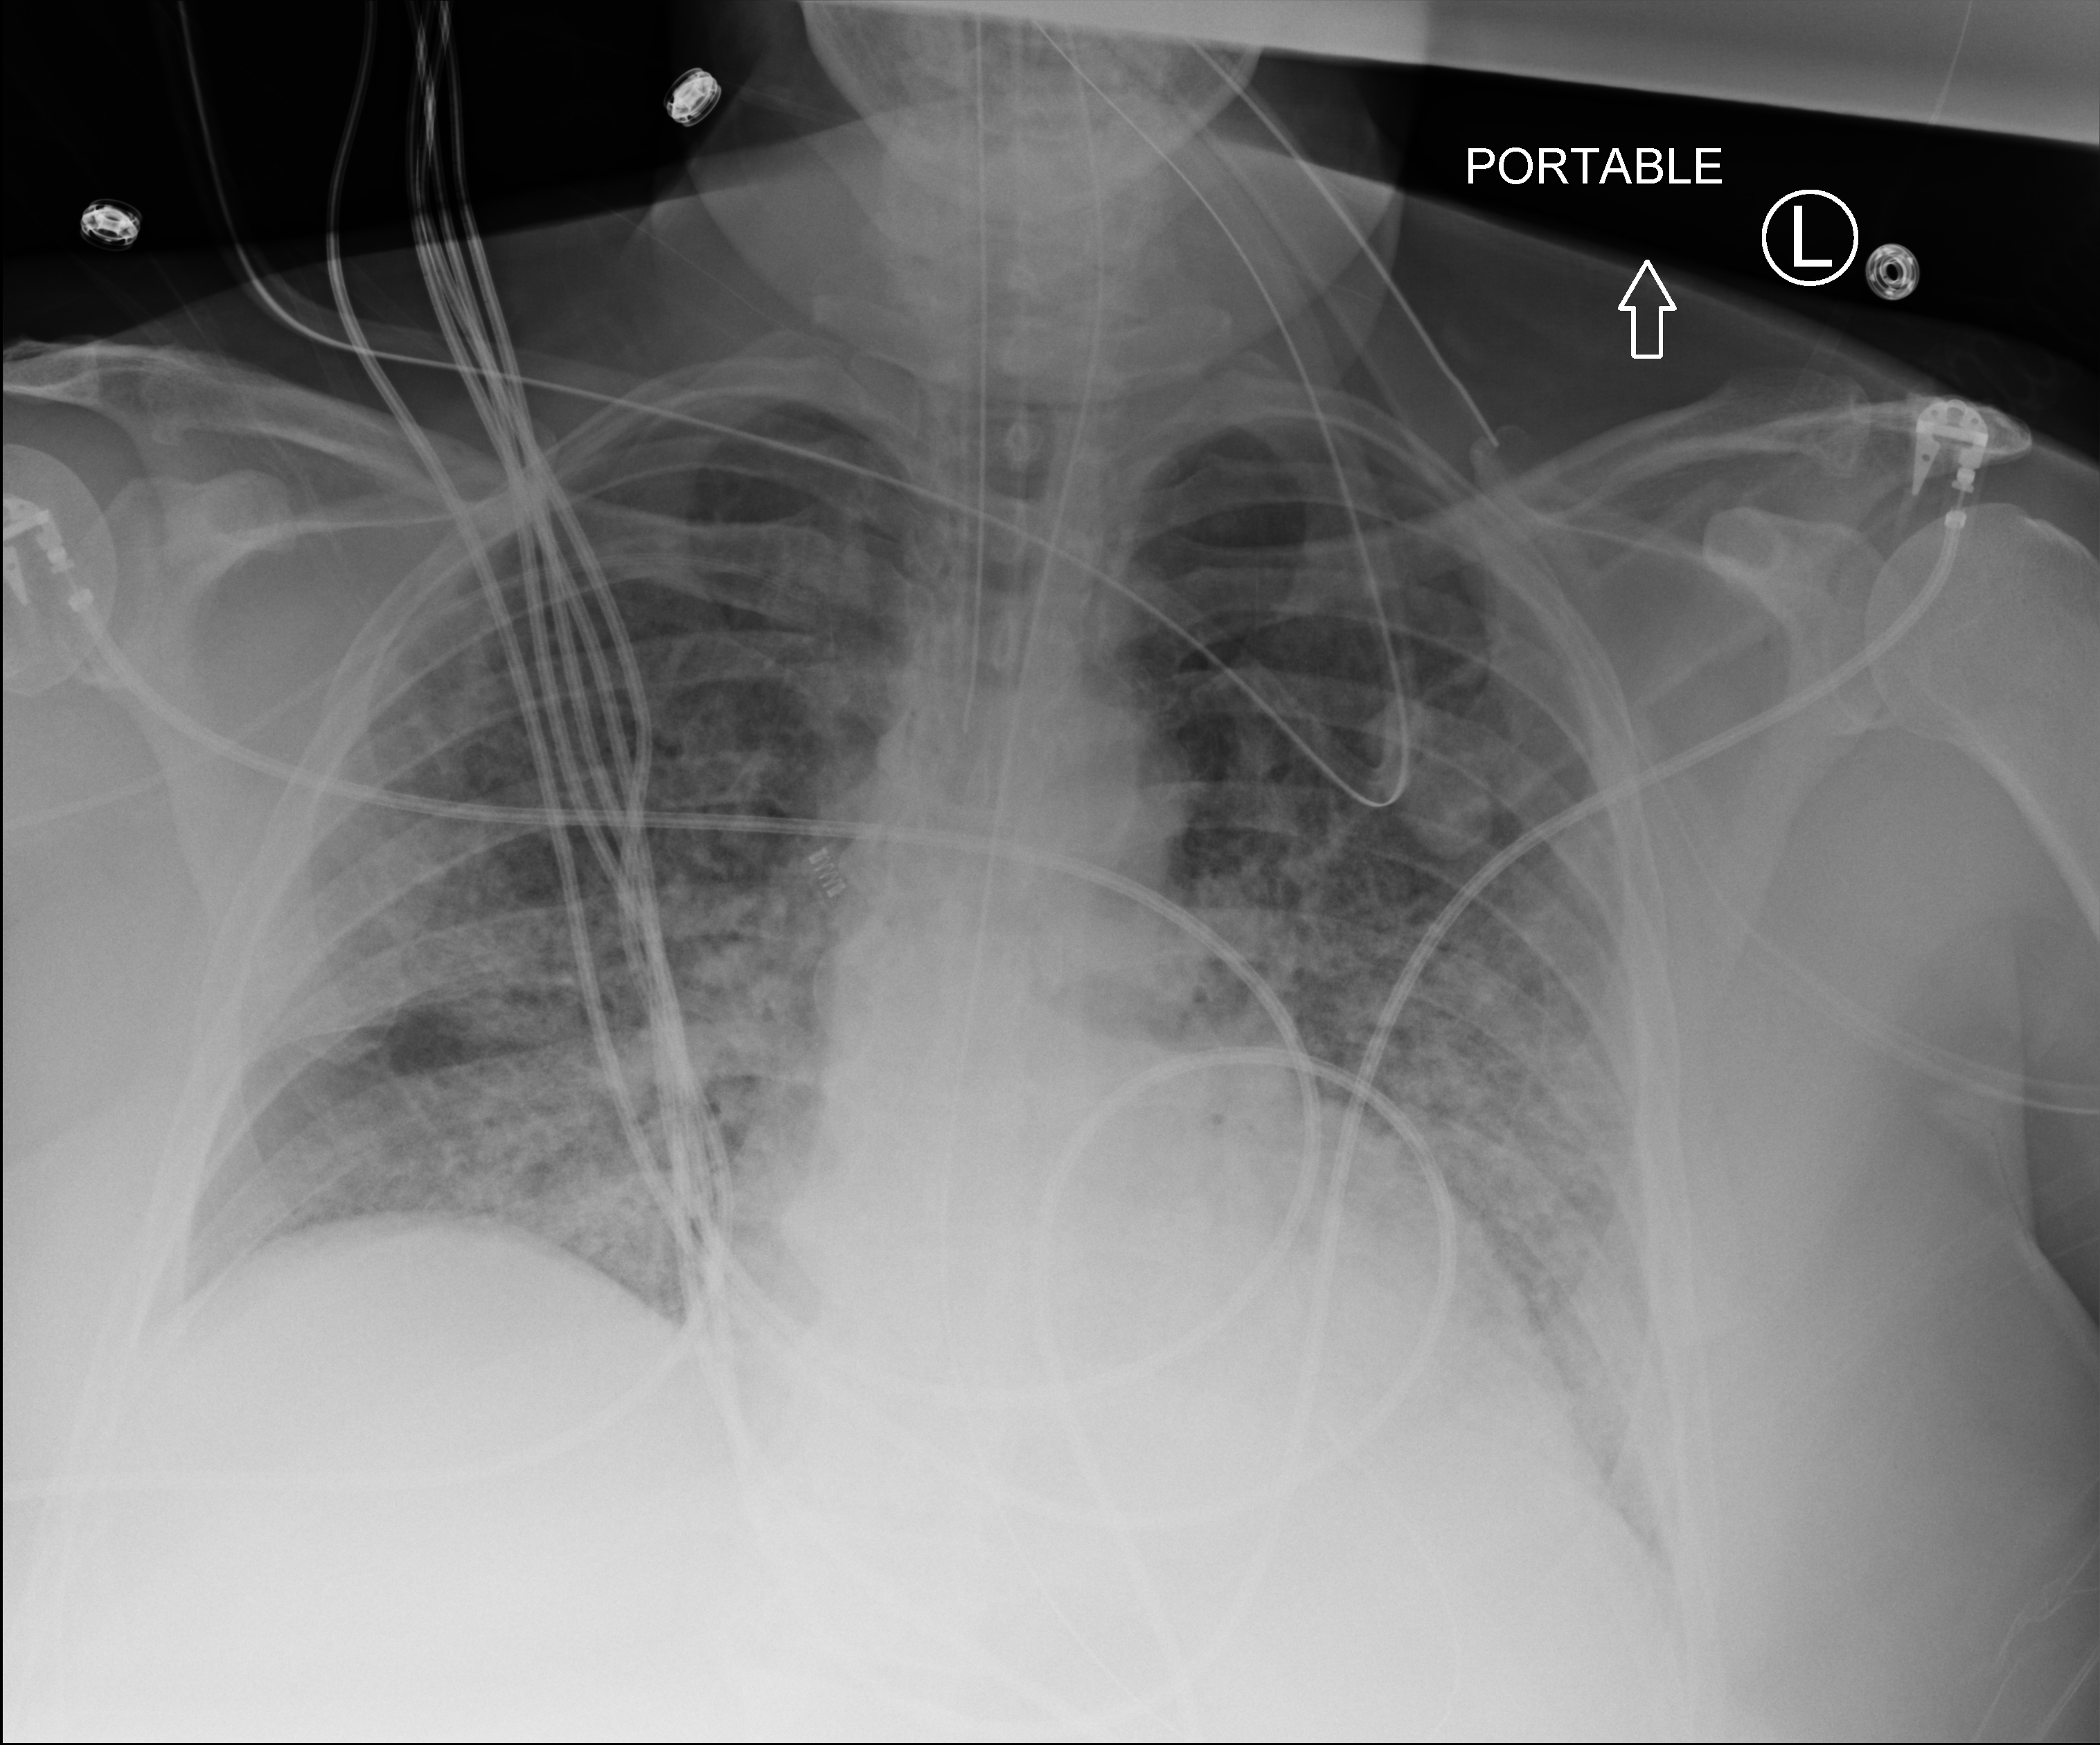
Portable chest radiograph, anteroposterior (AP) projection. Patient hospitalised with COVID-19, aged 18–59 years.
Hospital-stay facts (about this admission, not read from this image; timing relative to this image not recorded): mechanically ventilated during this hospital stay: yes; admitted to intensive care during this hospital stay: yes.